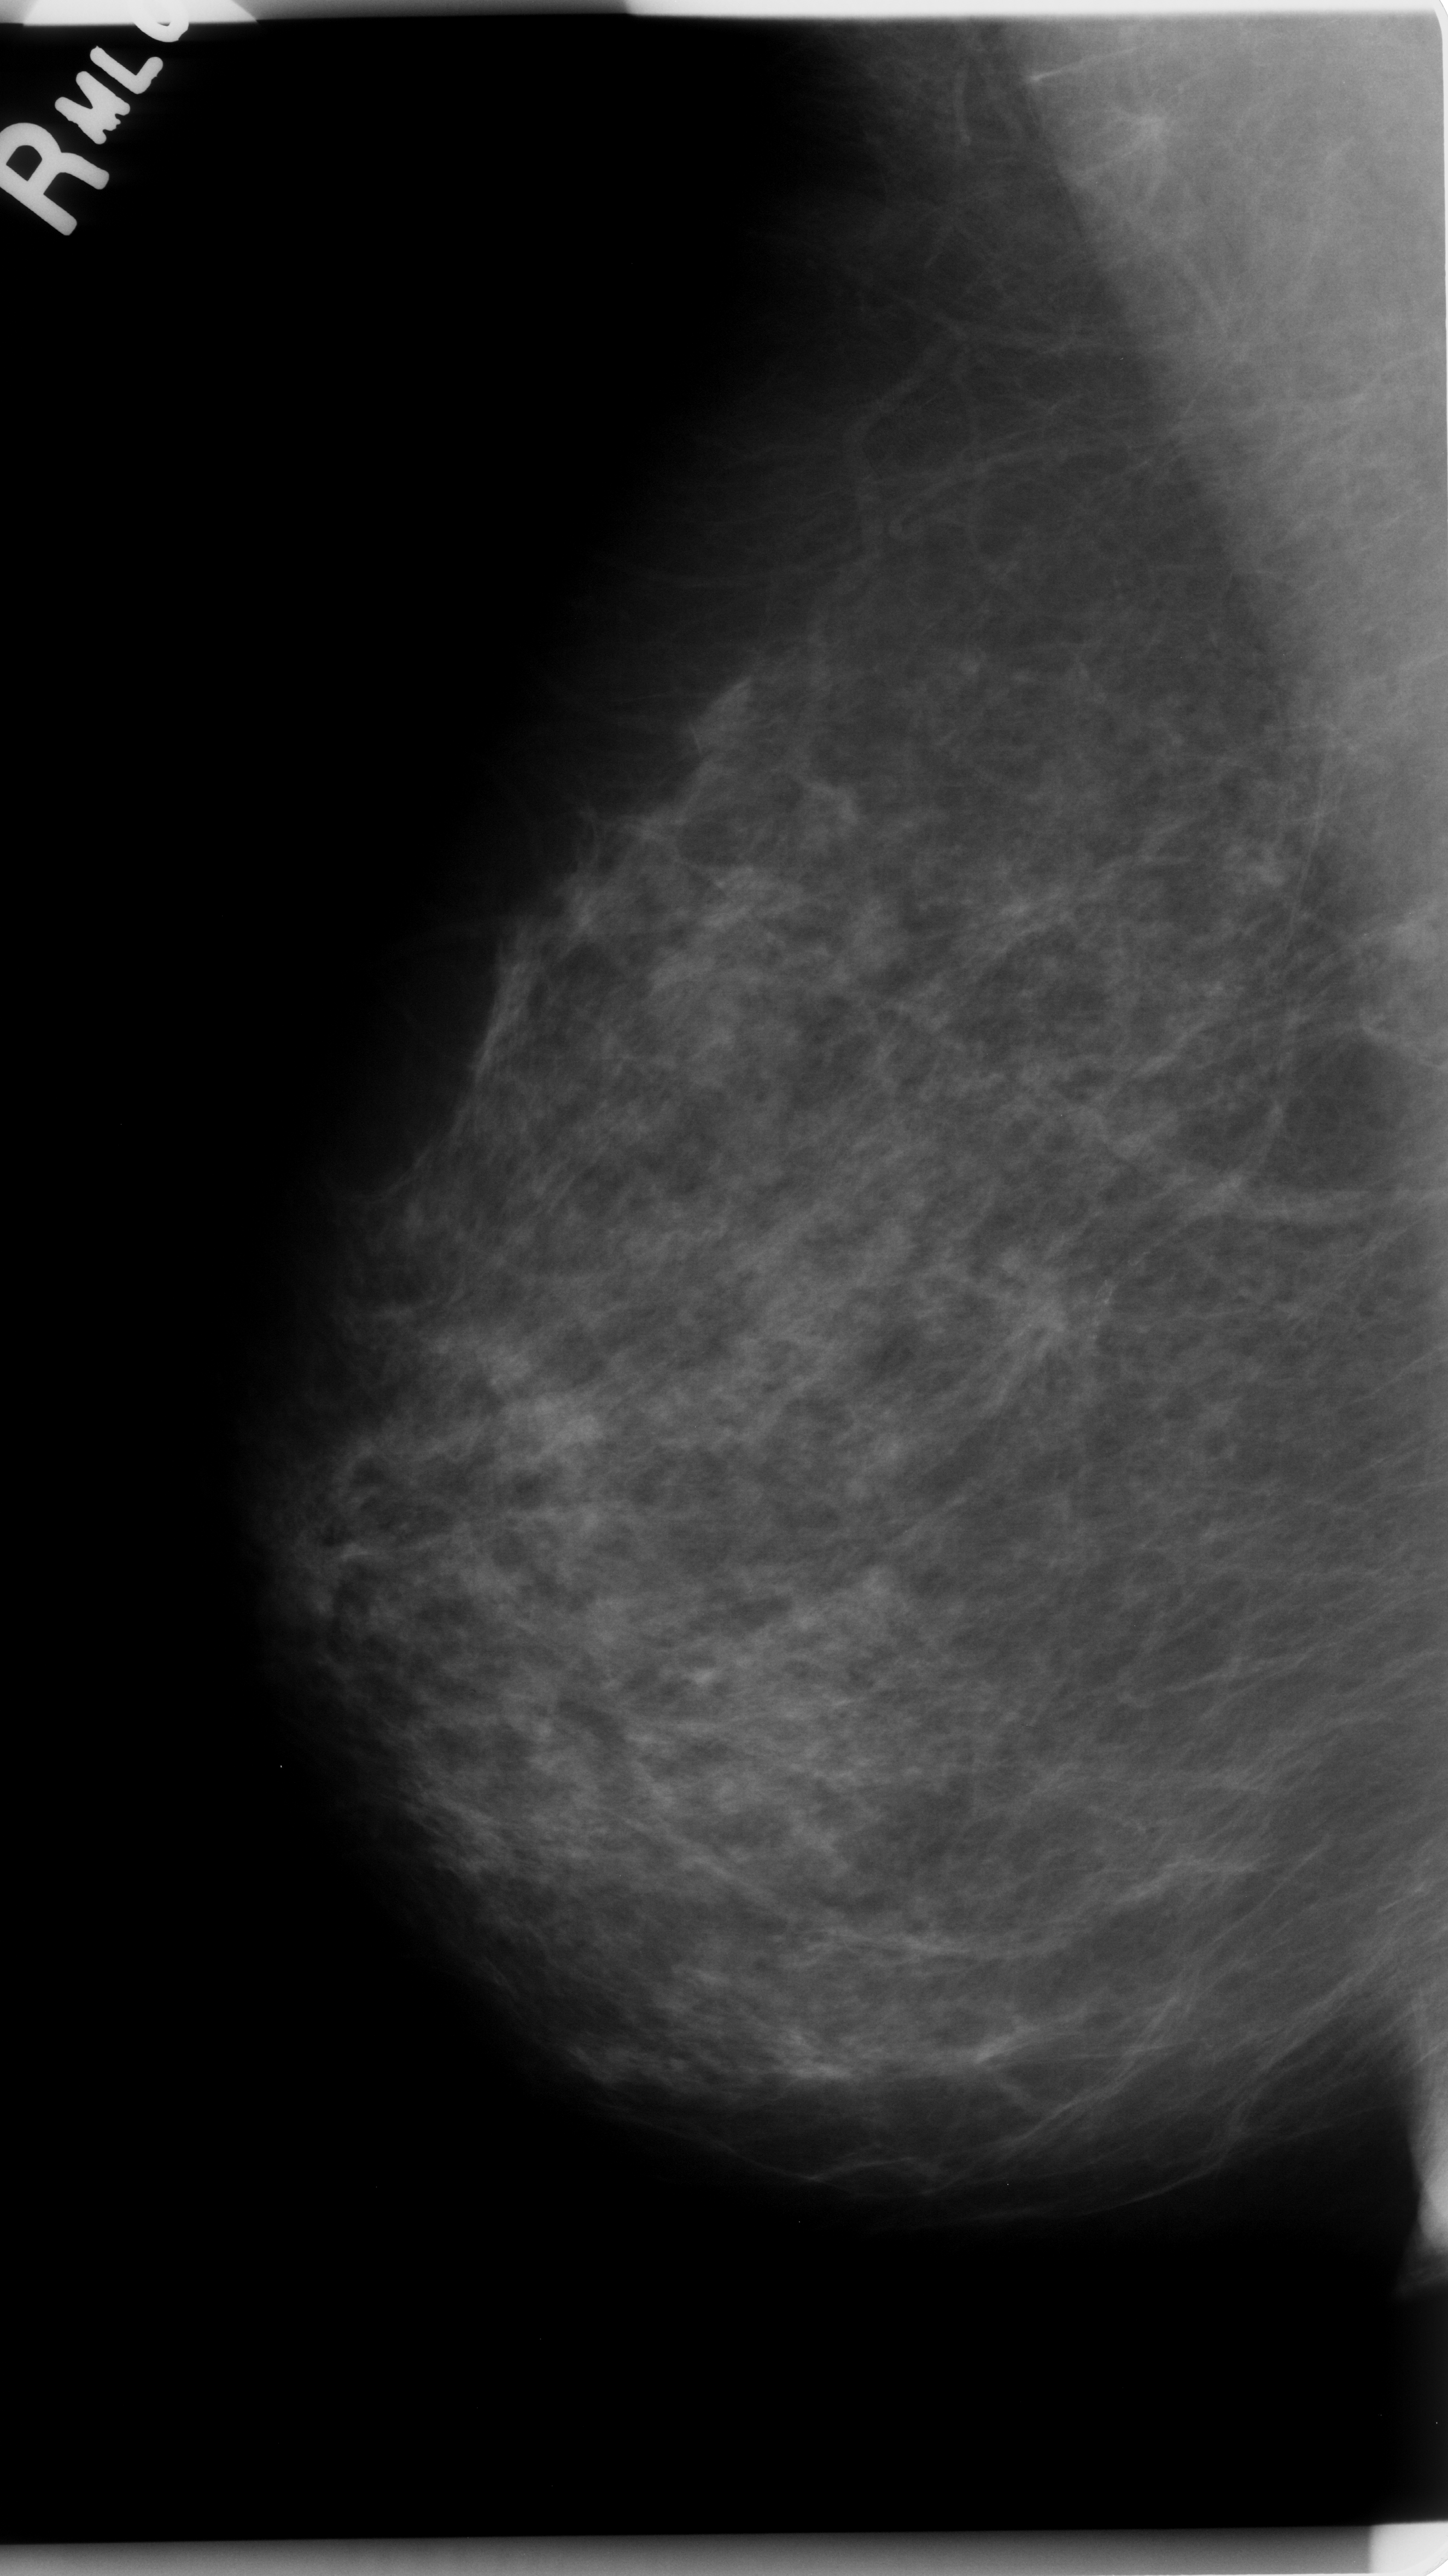
Digitized screen-film mammogram. Right breast. Mediolateral oblique (MLO) view. Breast composition: scattered fibroglandular densities (BI-RADS density category 2 of 4). 1448 × 2576 image matrix.
Marked abnormalities (boxes around the expert regions of interest):
- mass, shape architectural distortion, margins ill defined; BI-RADS assessment category 5; subtlety rating 4 on a 1 (subtle) to 5 (obvious) scale; pathology (as recorded): malignant: bounding box [x1, y1, x2, y2] px = [956, 1237, 1116, 1395]